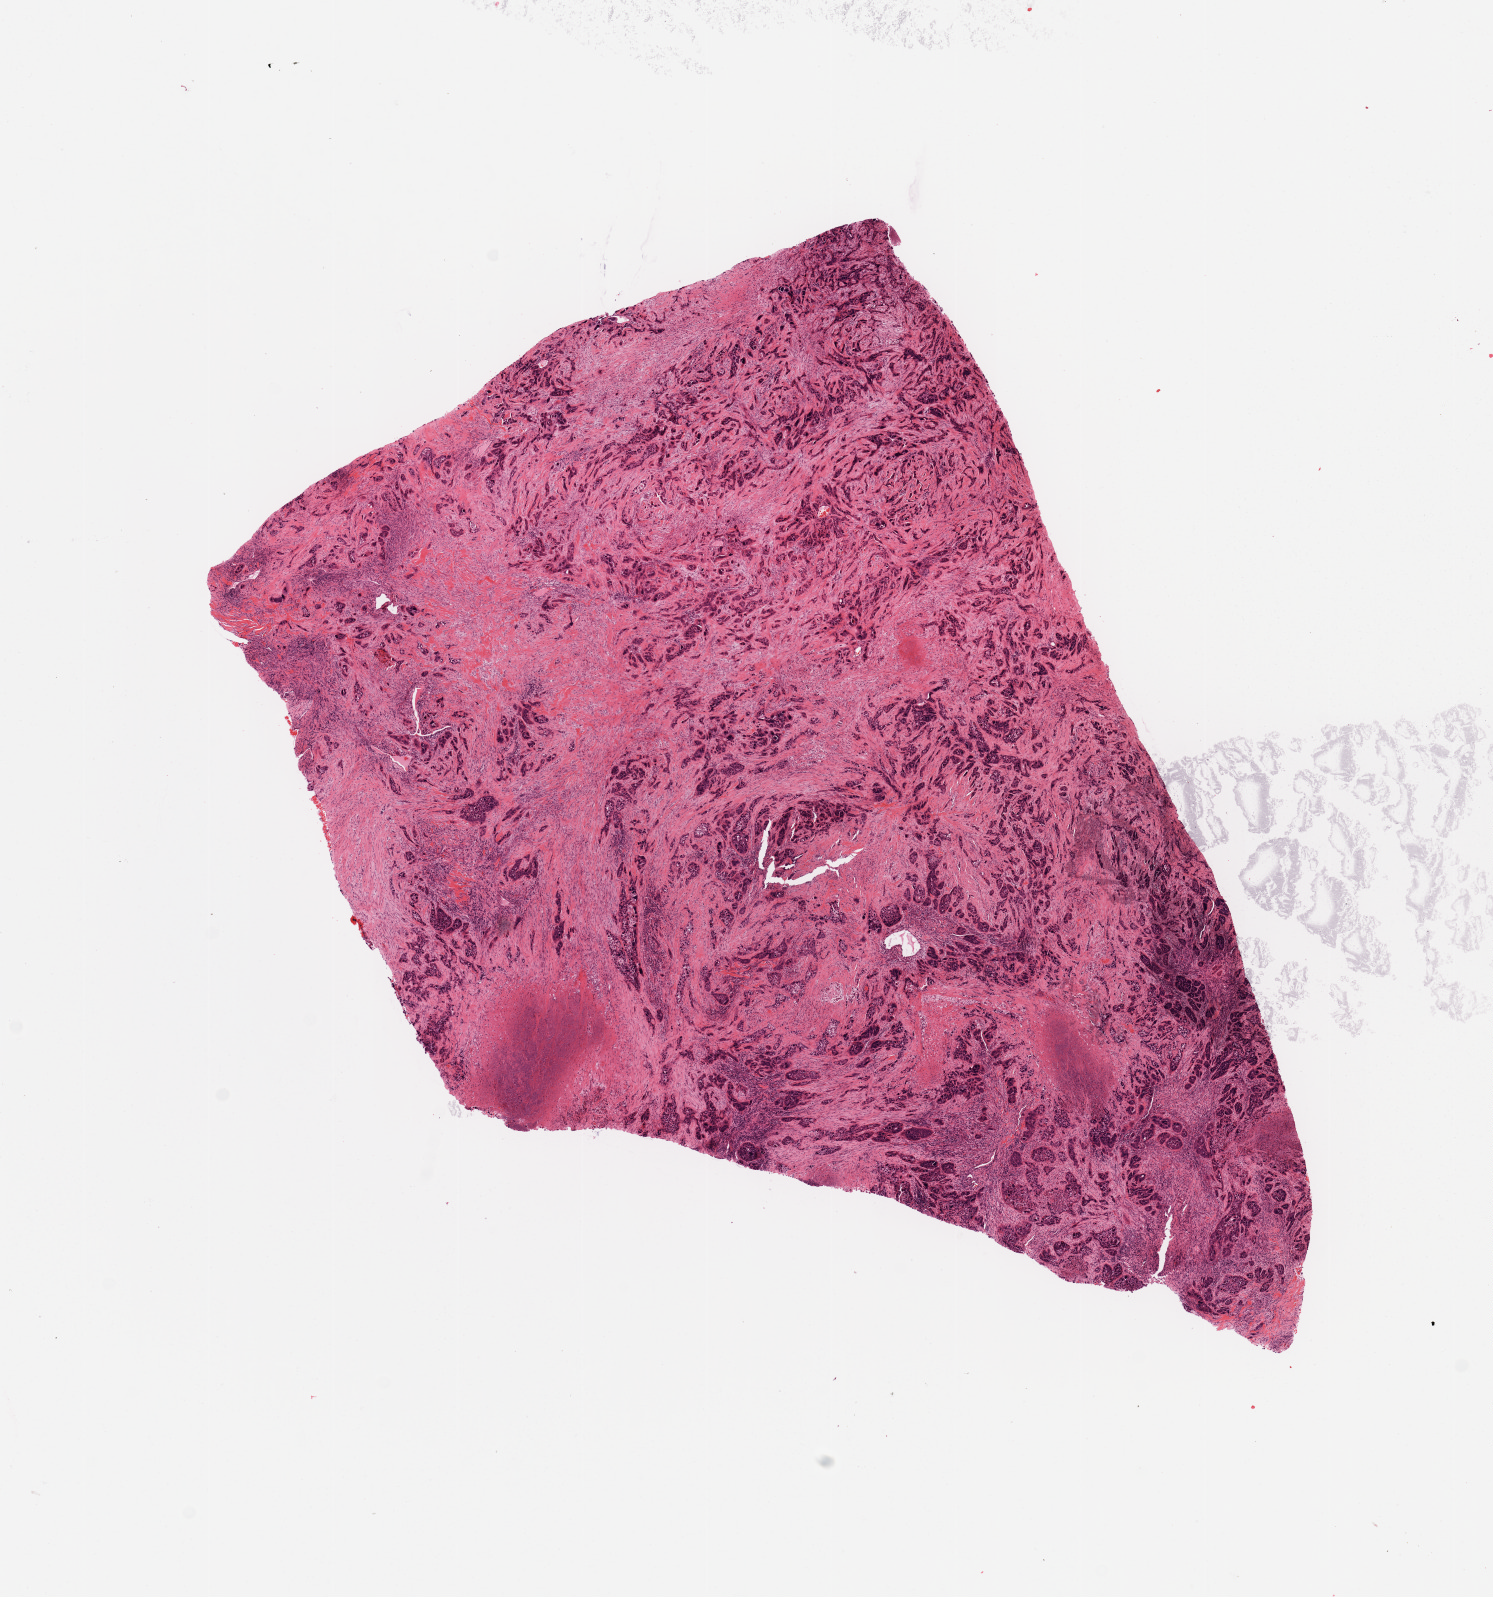
H&E-stained whole-slide image — low-resolution overview of the scanned area, about 11.8 x 12.6 mm, tumour tissue sample, sampled site: lung. Male, 66 y/o. Histologic grade: G3 (poorly differentiated). Pathologist review of this section (percent, as recorded): tumour nuclei 60%, necrosis 5%.
AJCC pathologic stage: IIA. Primary tumour site (as recorded): right upper lobe. Histologic diagnosis: Adenocarcinoma, NOS.